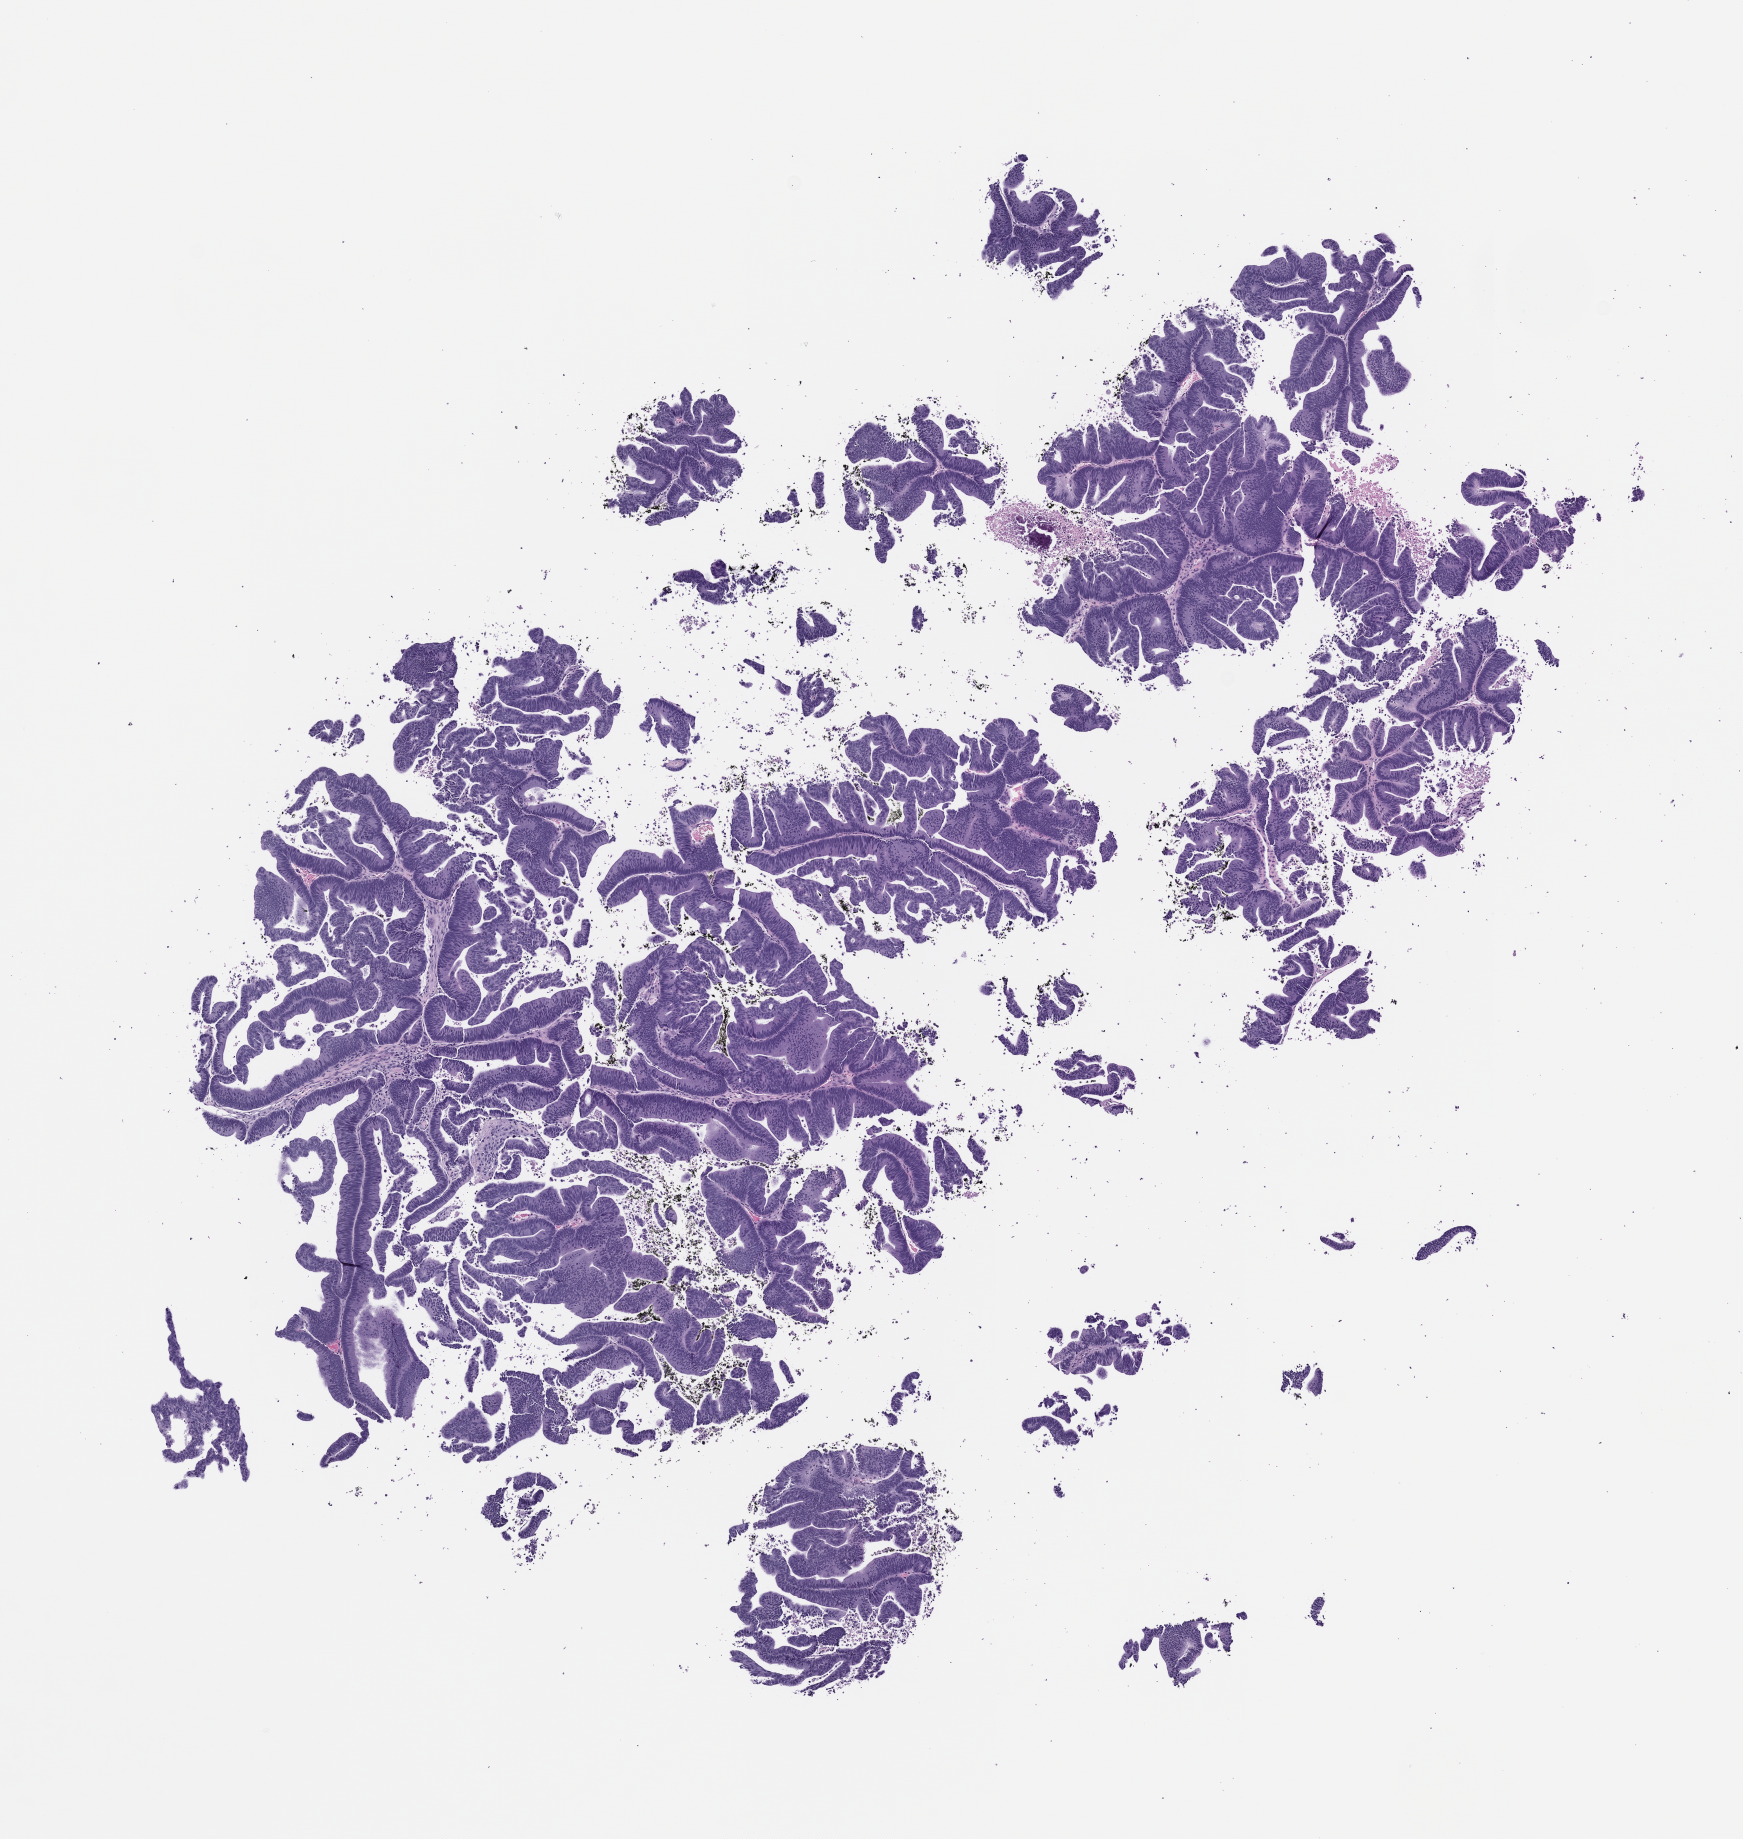
Whole-slide image, hematoxylin and eosin (H&E): patient-derived xenograft (human tumor grown in a mouse), passage 3 — low-resolution overview of the scanned area, about 7.0 x 7.4 mm, formalin-fixed paraffin-embedded section, tumor site category: gastrointestinal tract.
• originating patient diagnosis: Colorectal Carcinoma